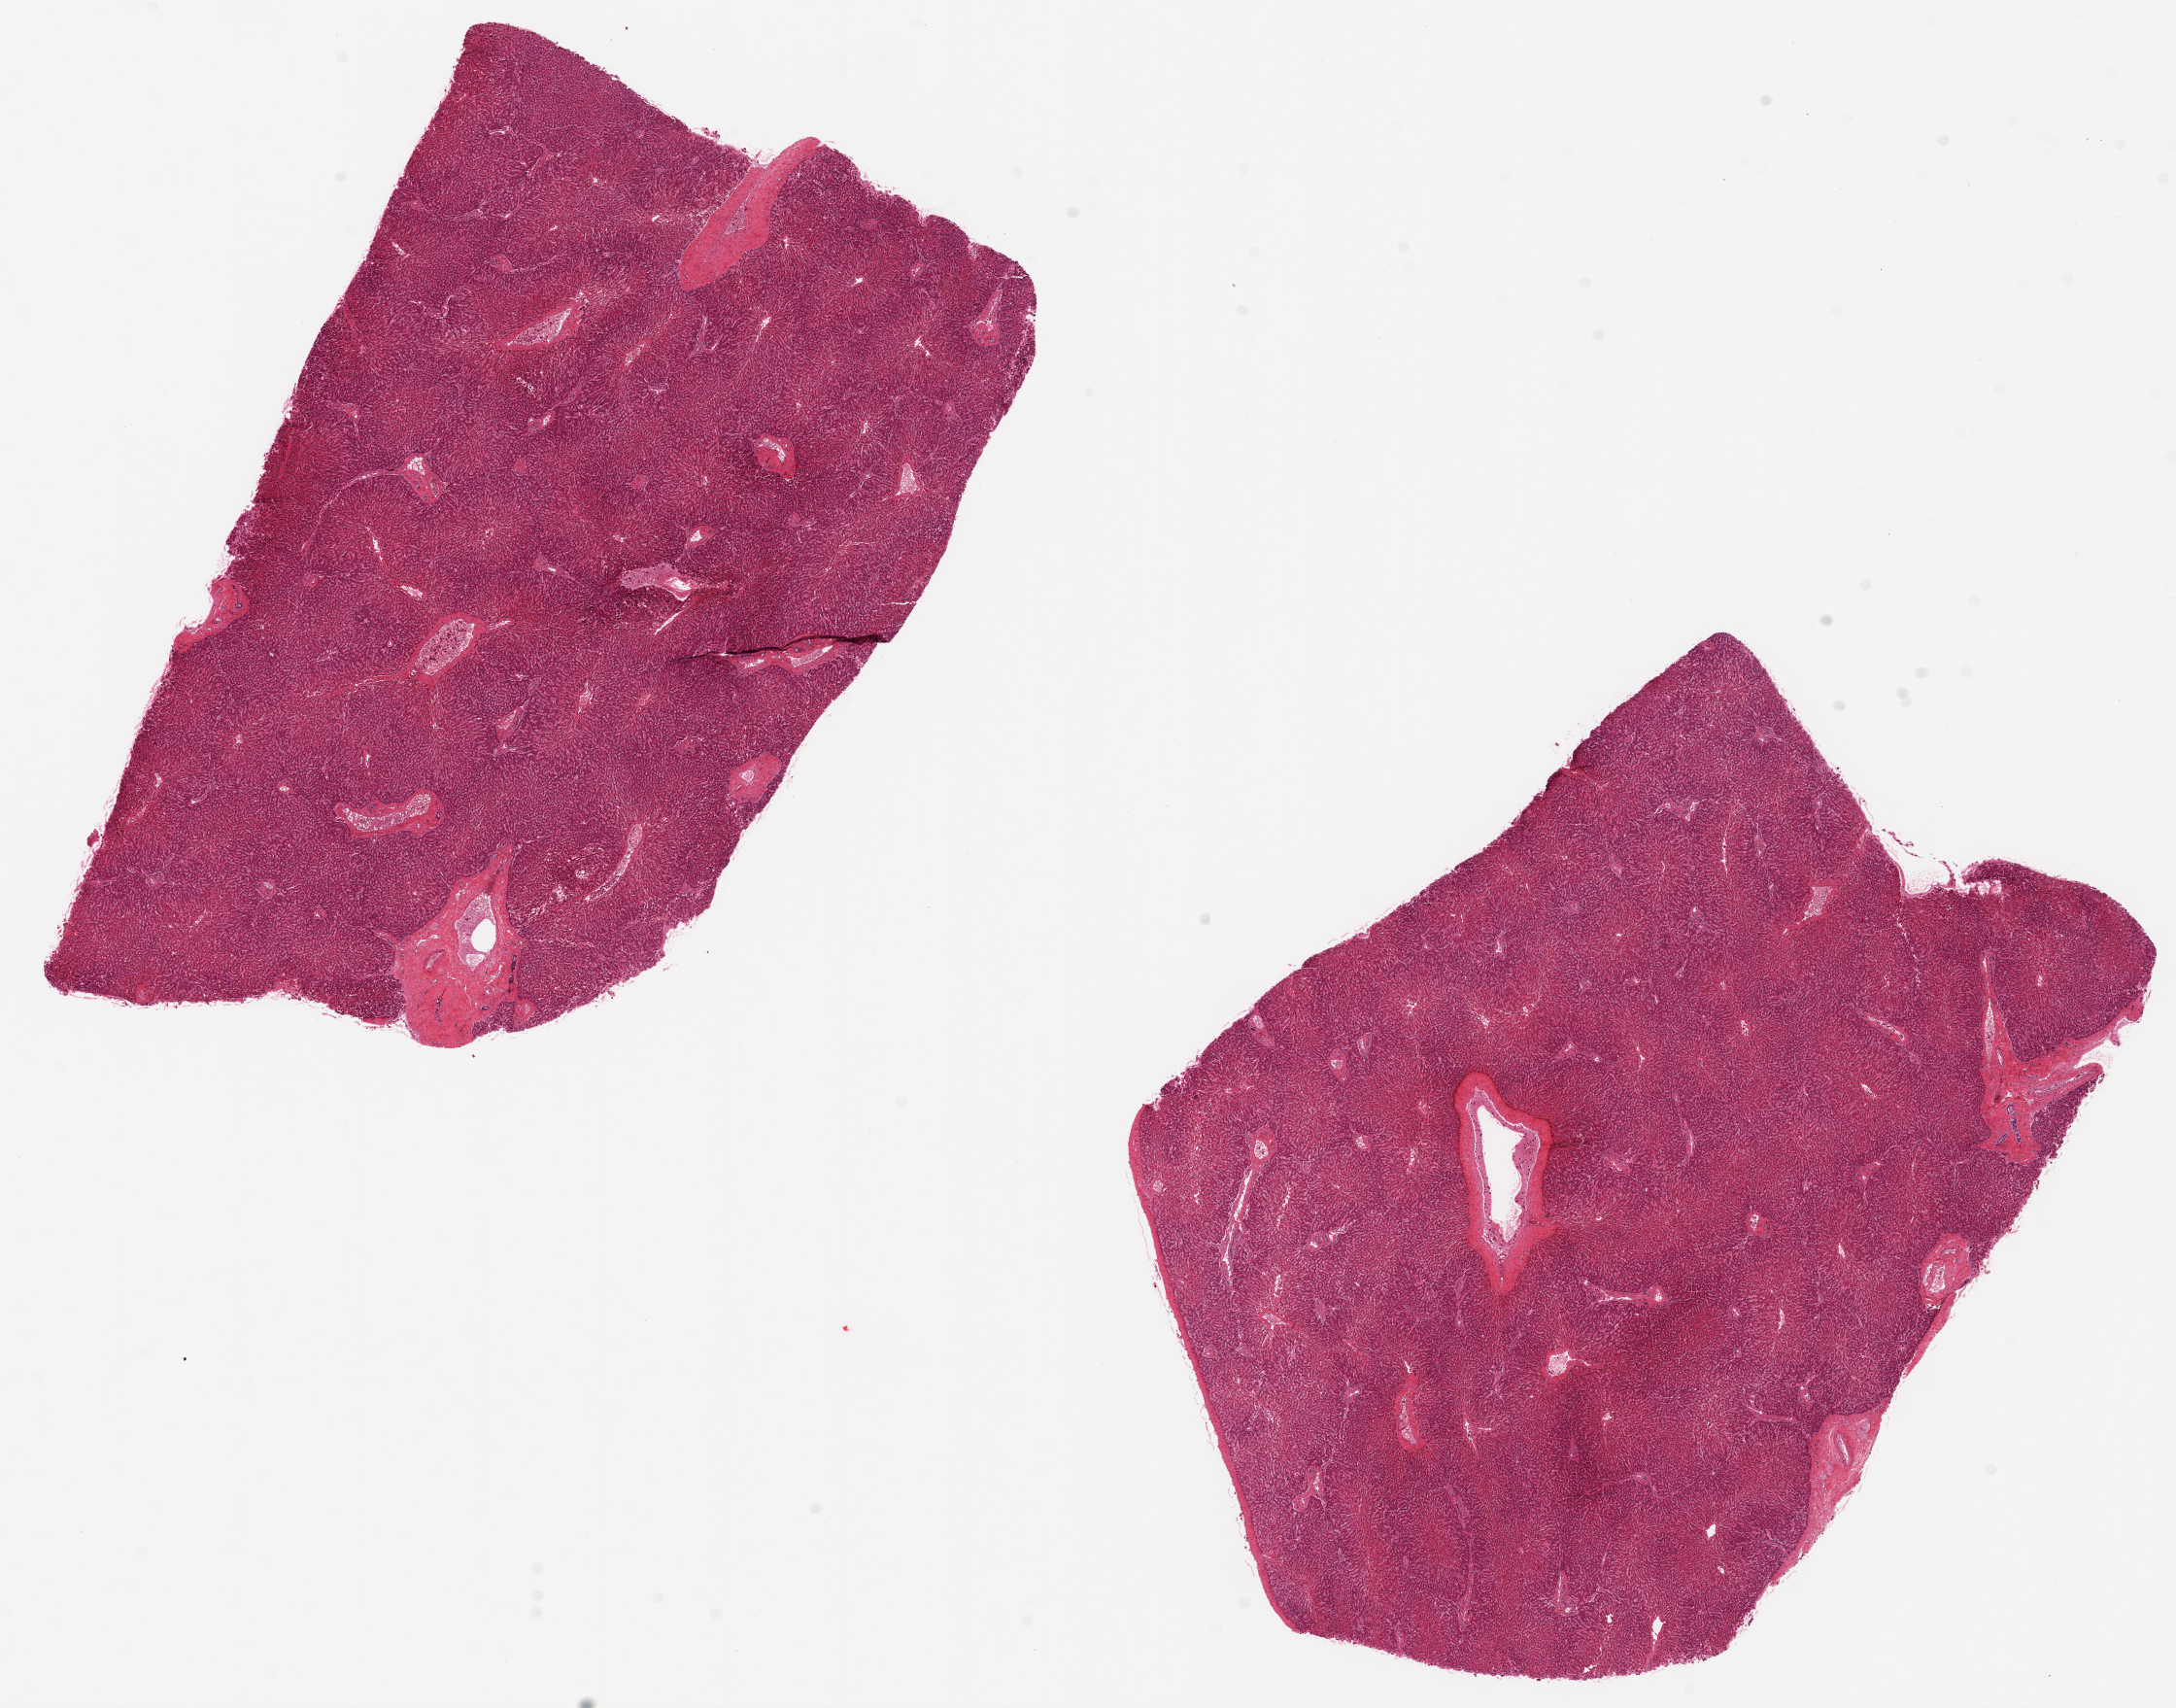
Whole-slide image, haematoxylin and eosin stain, brightfield, low-resolution overview of the scanned area, about 17.7 x 13.9 mm; PAXgene-fixed, paraffin-embedded tissue; sampled site (target tissue): liver; tissue donor sample. Male donor.
Reviewer comment on this tissue sample: 2 pieces ~7x5mm. No steatosis, moderately autolyzed.